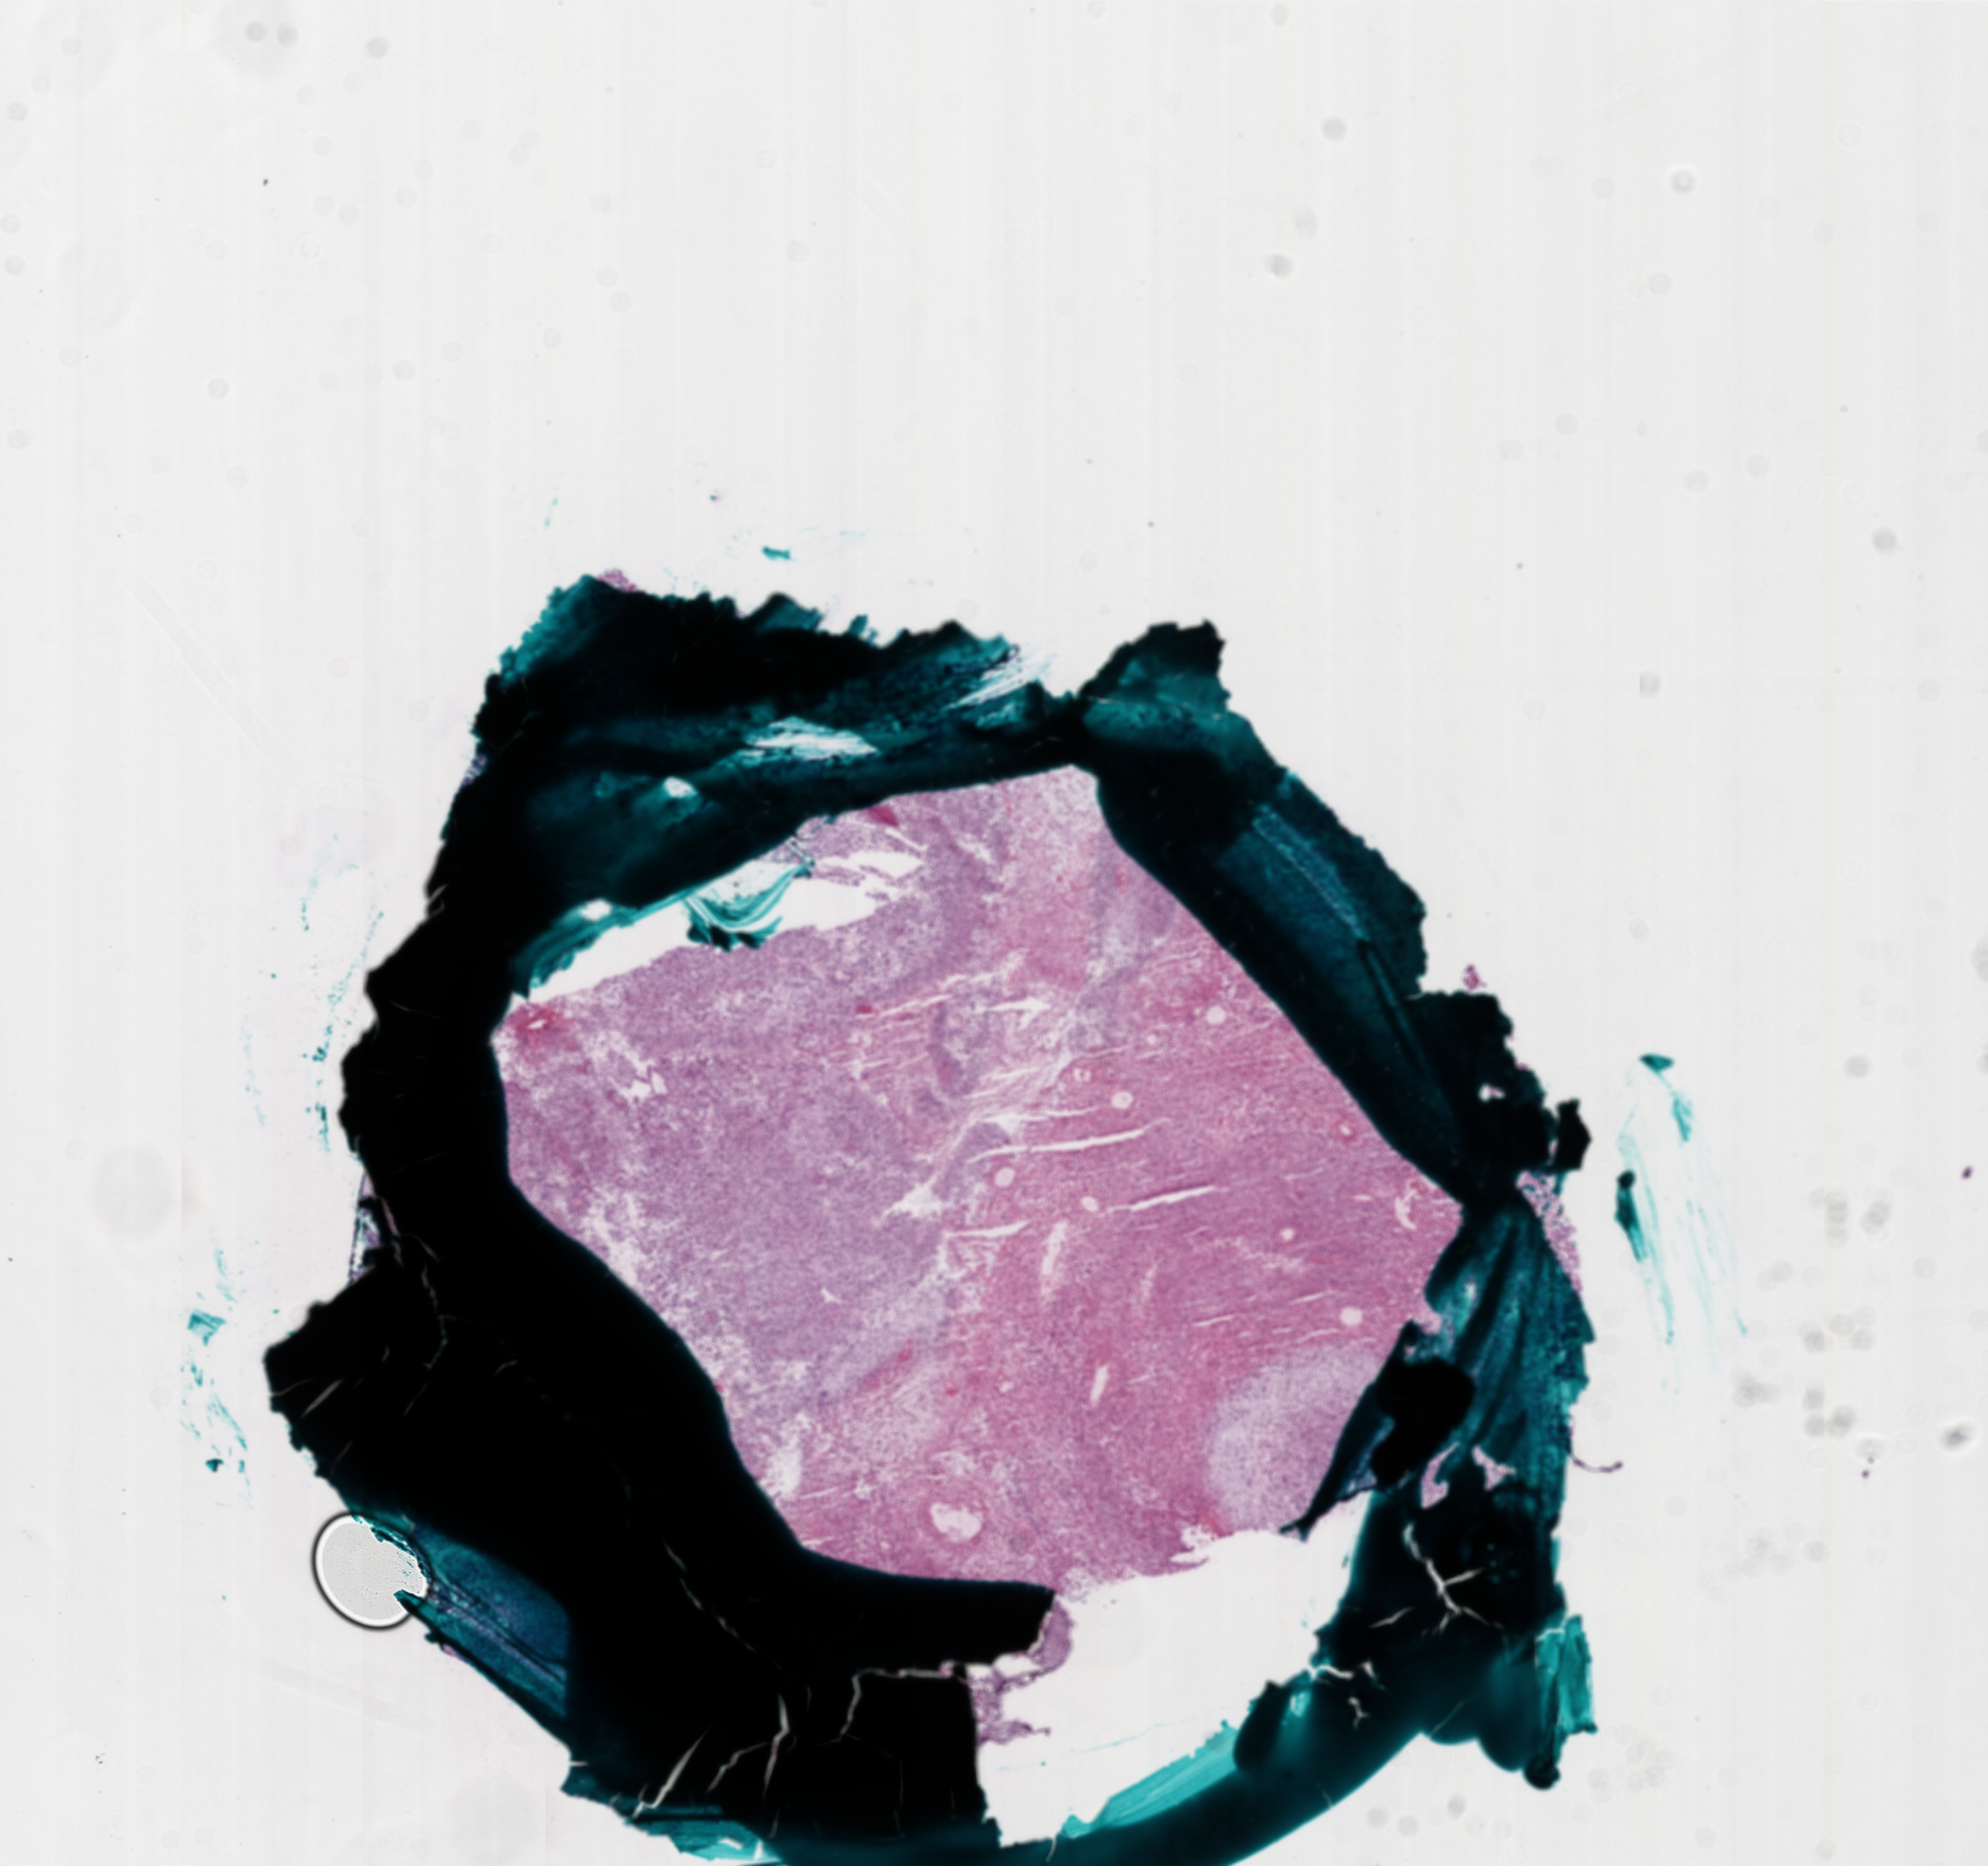
Digitized H&E-stained tissue section (whole slide), whole scanned area (about 11.0 x 10.3 mm, slide scanned at 20x) shown as a low-resolution overview; frozen section from the bottom of the tissue portion; sample: primary tumour, brain. Male patient; age at initial diagnosis 62 years. Composition of this section per pathologist review: tumour cells 60%, tumour nuclei 100%, normal cells 0%, stromal cells 0%, necrosis 40%.
• histologic diagnosis: Glioblastoma